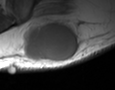
MRI of an extremity soft-tissue mass, one axial slice. Slice 20 of 35 in the series (ordered by position). MR volume resampled by the dataset authors to the PET/CT grid (not the native acquisition matrix). 3.27 mm slice thickness. 115 × 90 image matrix, field of view 112 × 88 mm. Male patient. Case-level facts recorded for this patient, not image findings: histological type: pleiomorphic leiomyosarcoma; grade: high; site of the primary tumour: left buttock.
Annotated regions visible in this slice (expert contour drawn on MRI and transferred to this co-registered scan by the dataset authors):
- gross tumour volume including surrounding oedema: box from (x=24, y=20) to (x=82, y=61) px
- gross tumour volume (mass): (x=24, y=23)–(x=79, y=61)